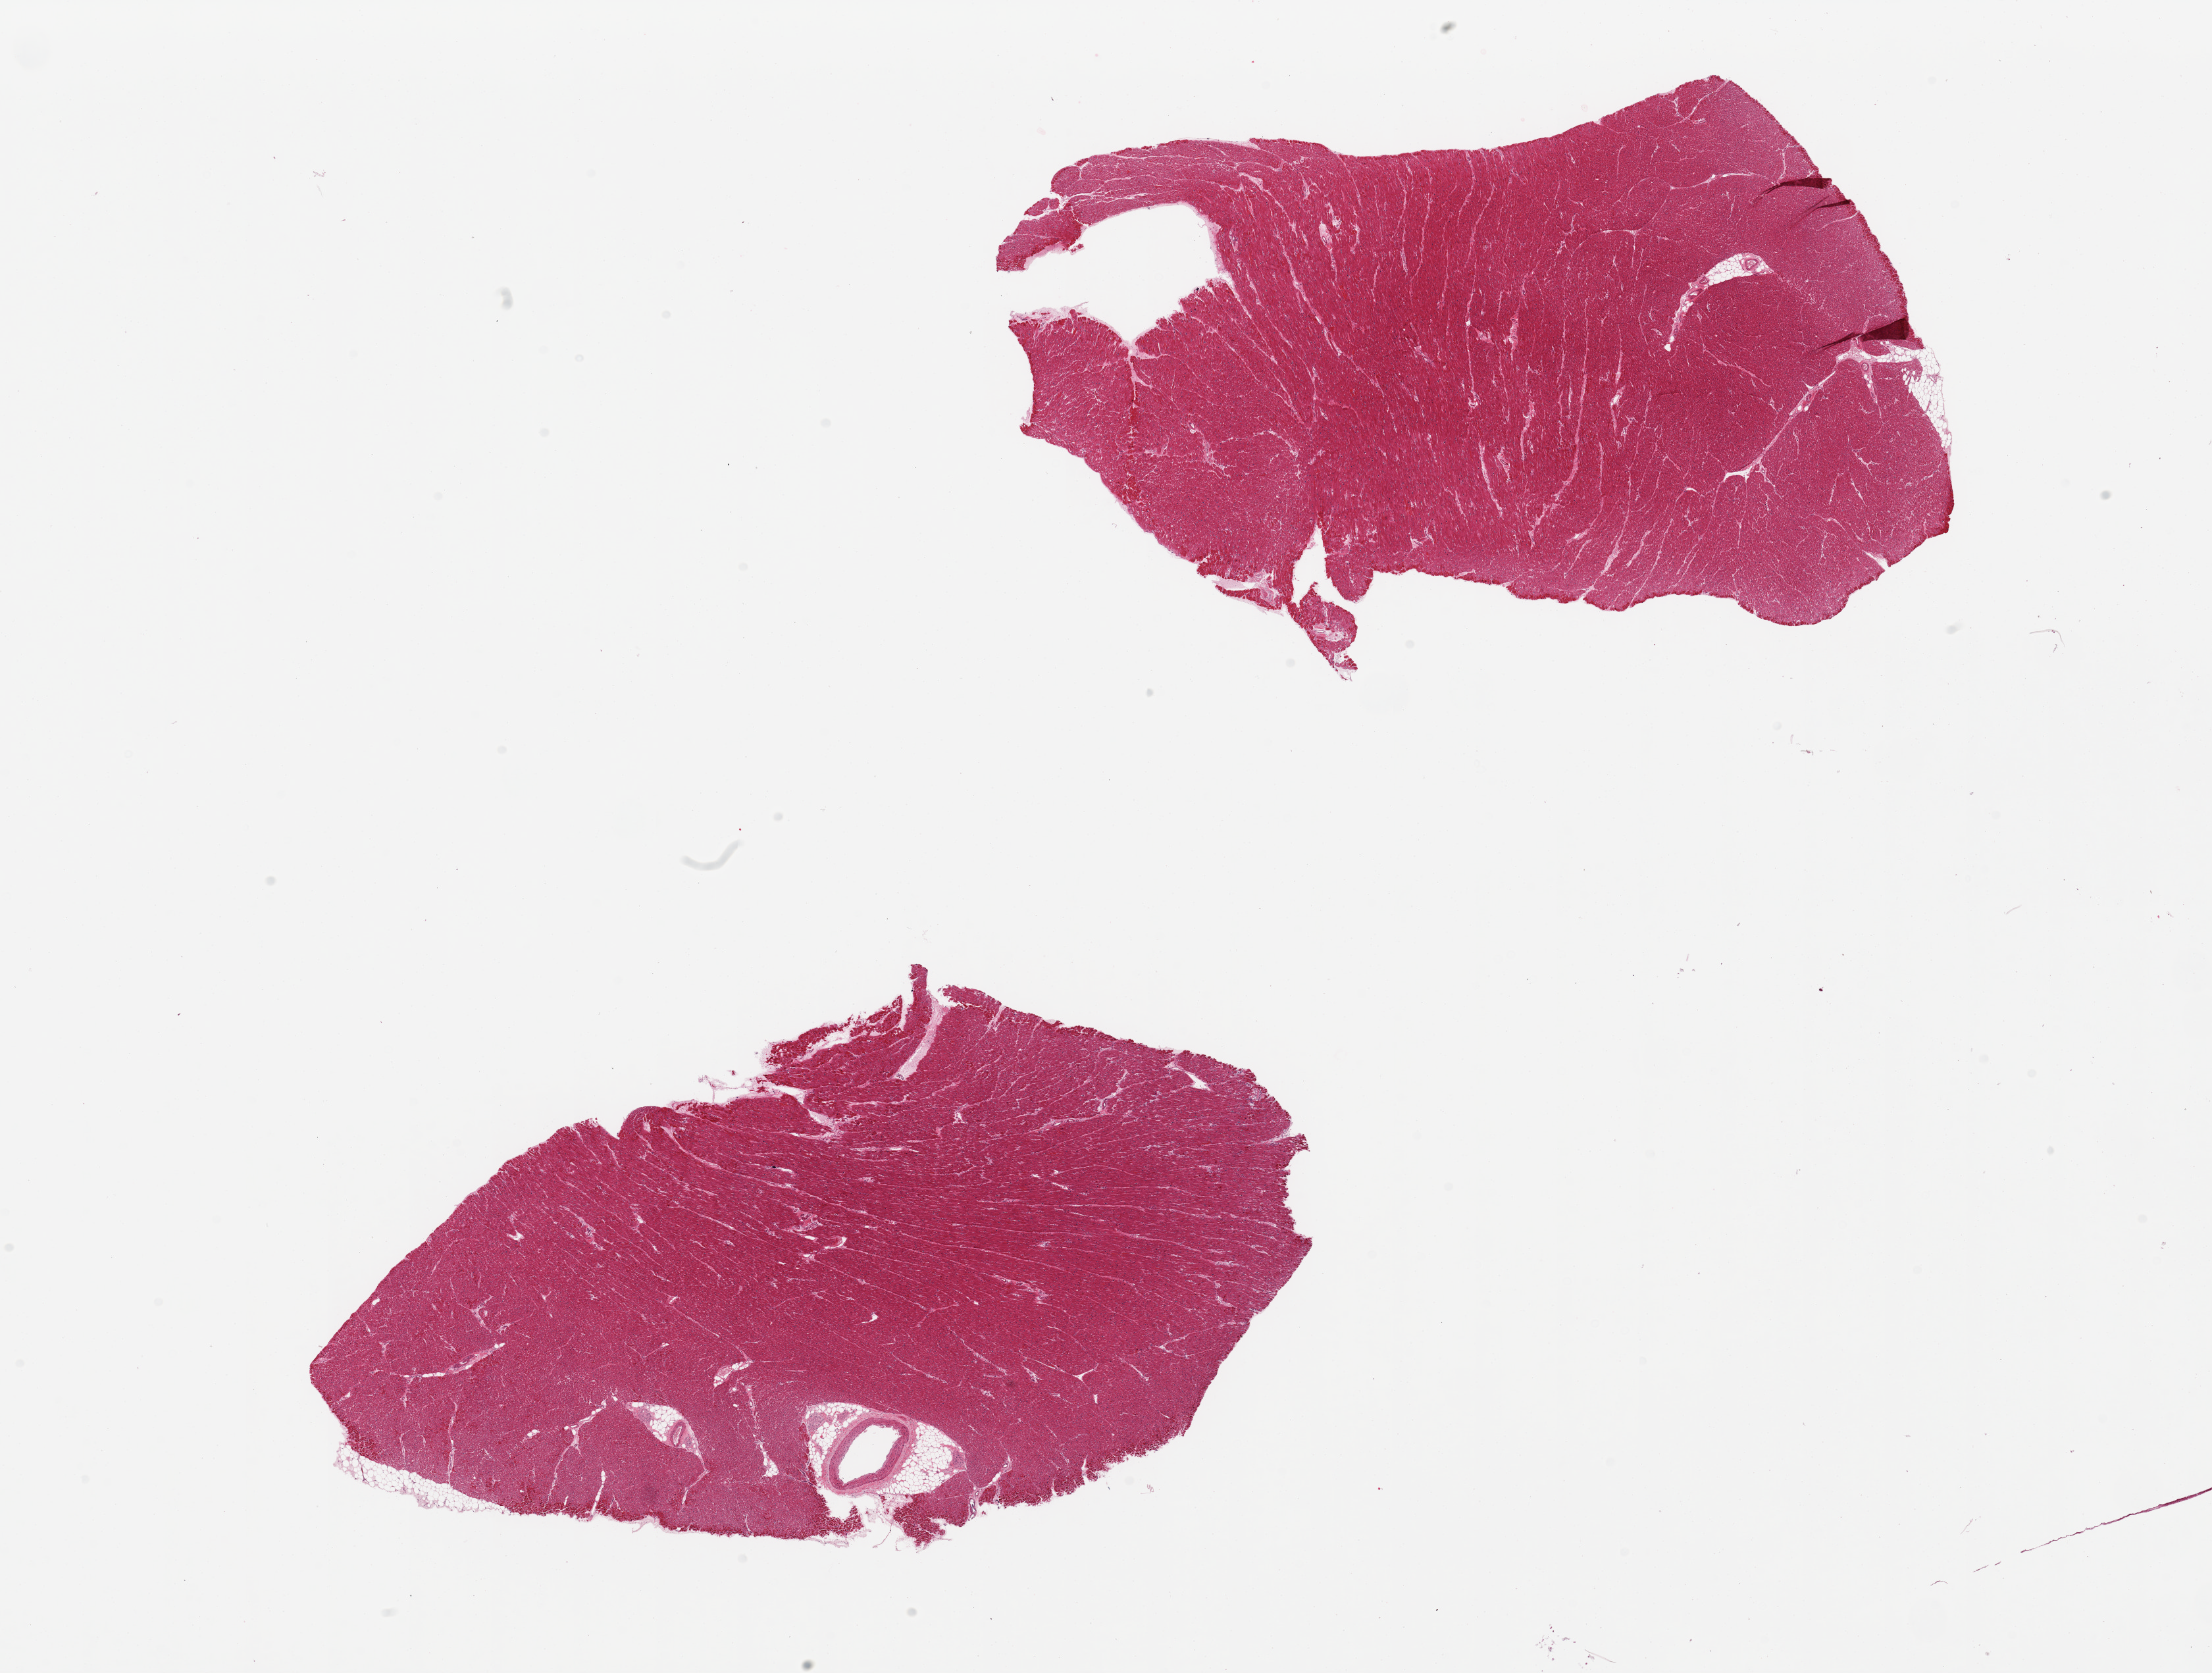
Digitized H&E-stained section — a low-resolution overview of the entire scanned area, about 26.6 x 20.1 mm, PAXgene-fixed paraffin-embedded (PFPE) section, target tissue: heart, donor tissue sample. Female donor.
Review note (as recorded): 2 pieces, mild ischemic changes; incidental 1mm coronary artery branch noted.